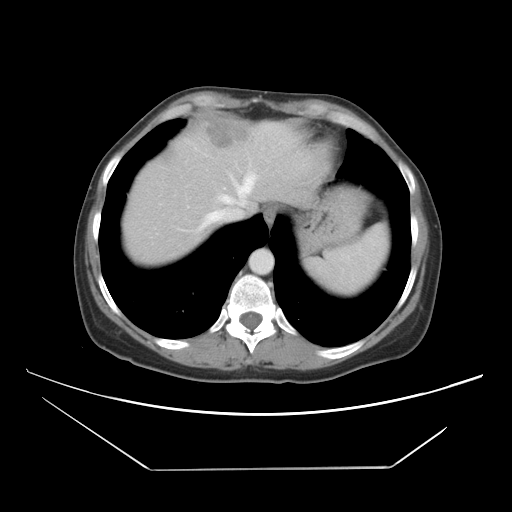
Contrast-enhanced abdominal CT, one axial slice. Slice 36 of 42 in the series (ordered by position). 120 kVp. Intravenous contrast given. Soft-tissue window (W 400 / L 40 HU). 5 mm slice thickness. 512 × 512 image matrix. Female patient, age 52 years. From the clinical record (not read from this slice): diagnosis: colorectal cancer liver metastases, imaged before liver resection; multiple liver metastases: yes; largest metastasis: 5.5 cm; chemotherapy before resection: yes.
Annotated regions visible in this slice (manually delineated by an expert):
- hepatic veins: bounding box [x1, y1, x2, y2] px = [200, 172, 257, 229]
- liver: [126, 123, 319, 263]
- planned liver remnant (the part of the liver to remain after resection): [135, 139, 224, 221]
- liver metastasis: [201, 125, 249, 148]